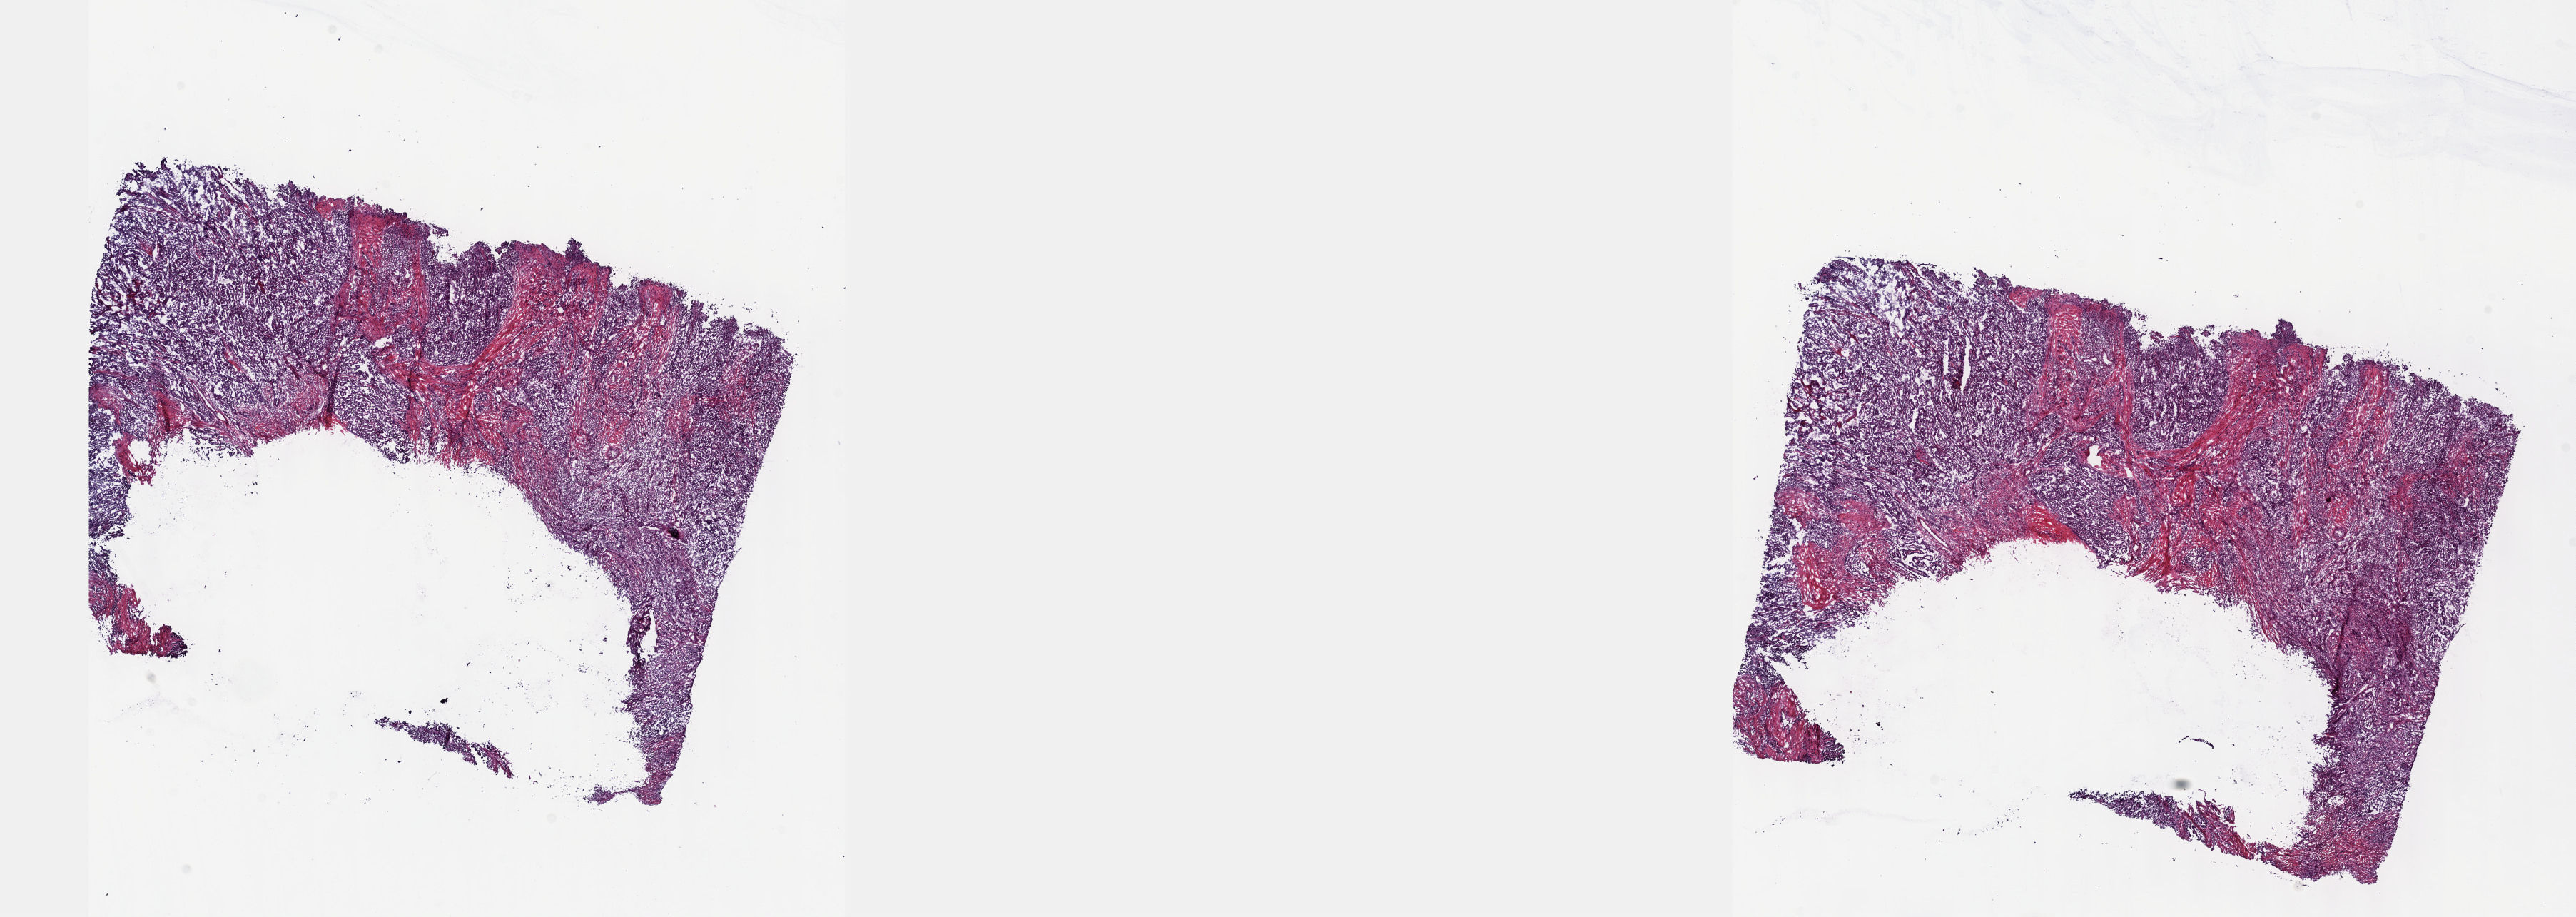
H&E whole-slide image, a low-resolution overview of the entire scanned area, about 29.2 x 10.4 mm, frozen section, thyroid, primary tumour sample. Female patient; age at initial diagnosis 74 years. Pathologist review of this section (percent, as recorded): tumour cells 80%, tumour nuclei 65%.
Pathologic diagnosis: Papillary carcinoma, NOS.